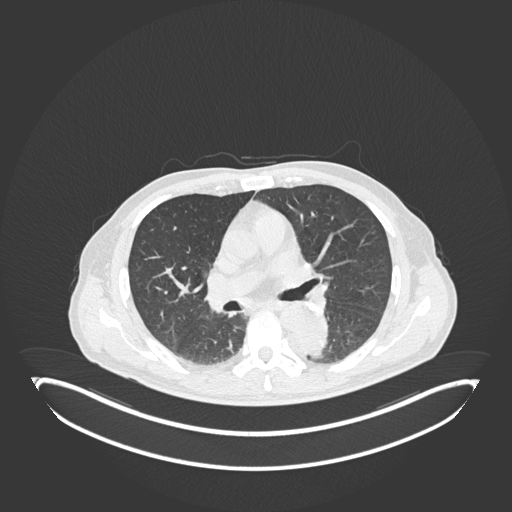
Chest CT, one axial slice; position 117 of 251 along the scan axis; reconstruction kernel B30f; 120 kVp; lung window (W 1500 / L -600 HU); 1 mm slice thickness; 512 × 512 image matrix. Patient: male, 72 years. Case-level facts recorded for this patient, not image findings: clinical TNM (as recorded): T2b N0 M1.
Structures marked on this image (rectangle marked by the reading radiologist):
- lung tumour (recorded histology: adenocarcinoma): box from (x=293, y=311) to (x=335, y=359) px